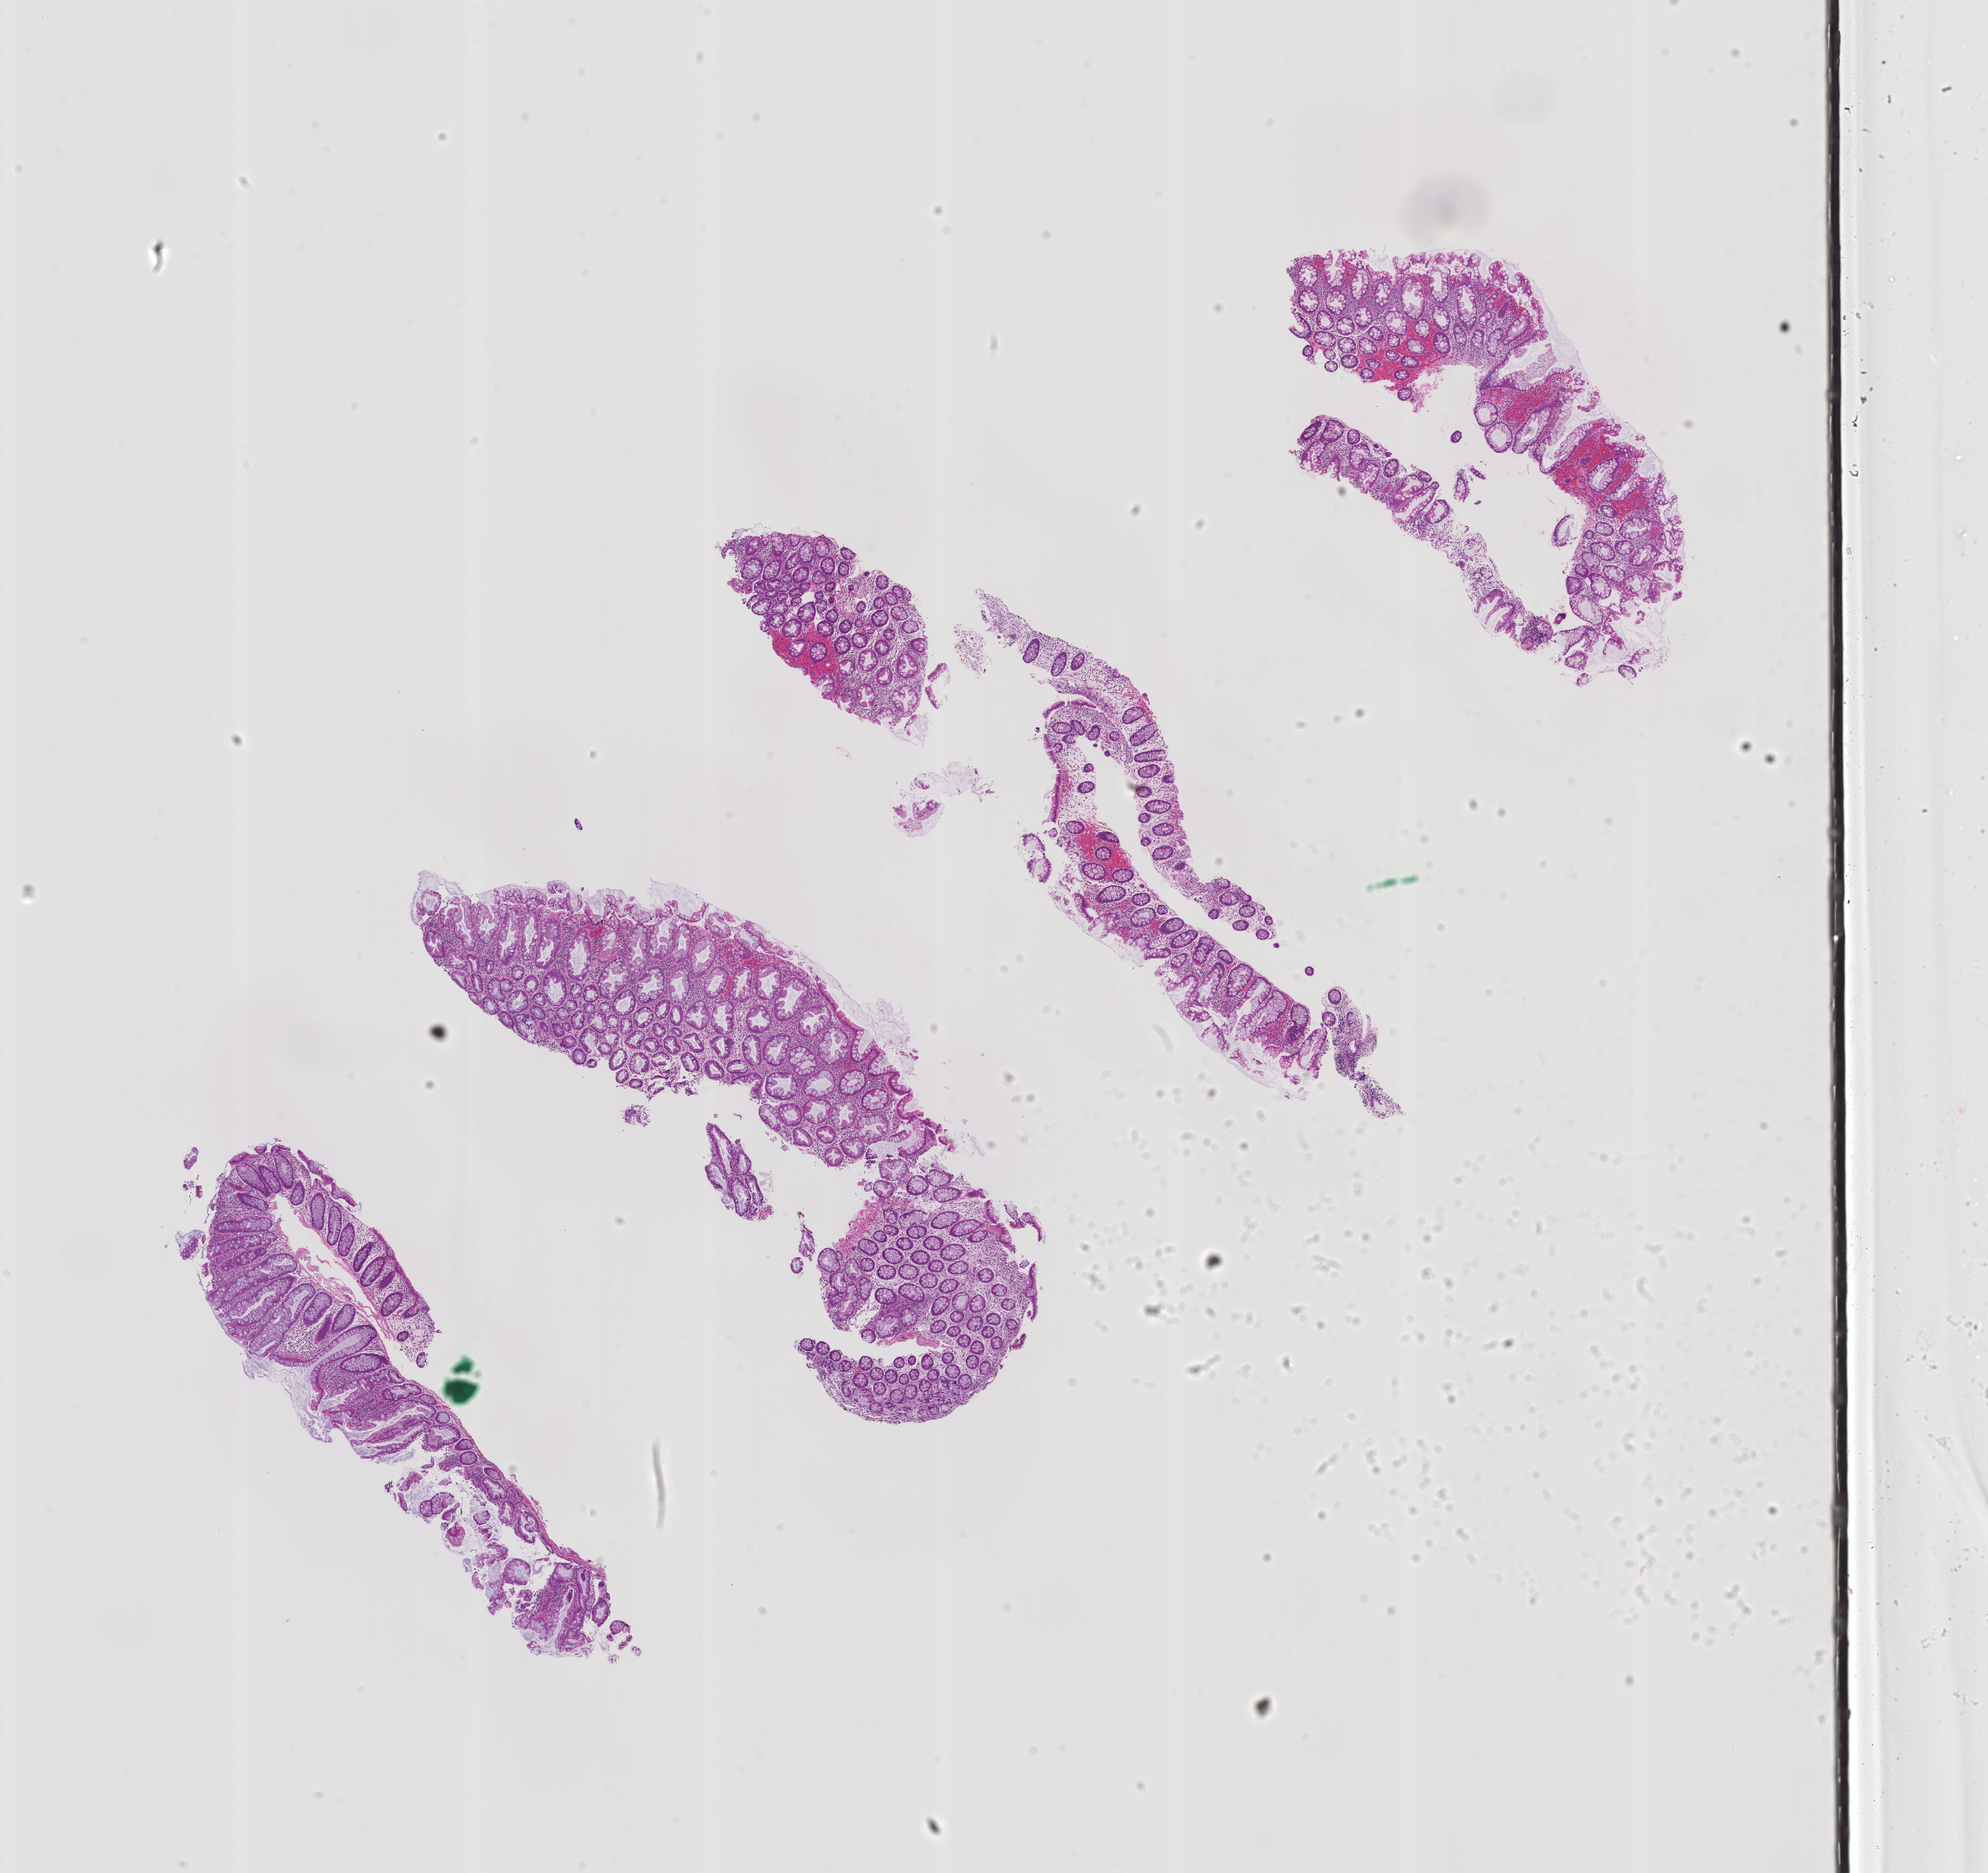
H&E whole-slide image of a colon biopsy — shown as a low-resolution overview of the whole scanned area (about 10.7 x 10.1 mm), FFPE section, descending colon. Male patient.
- lesion category (as recorded): premalignant